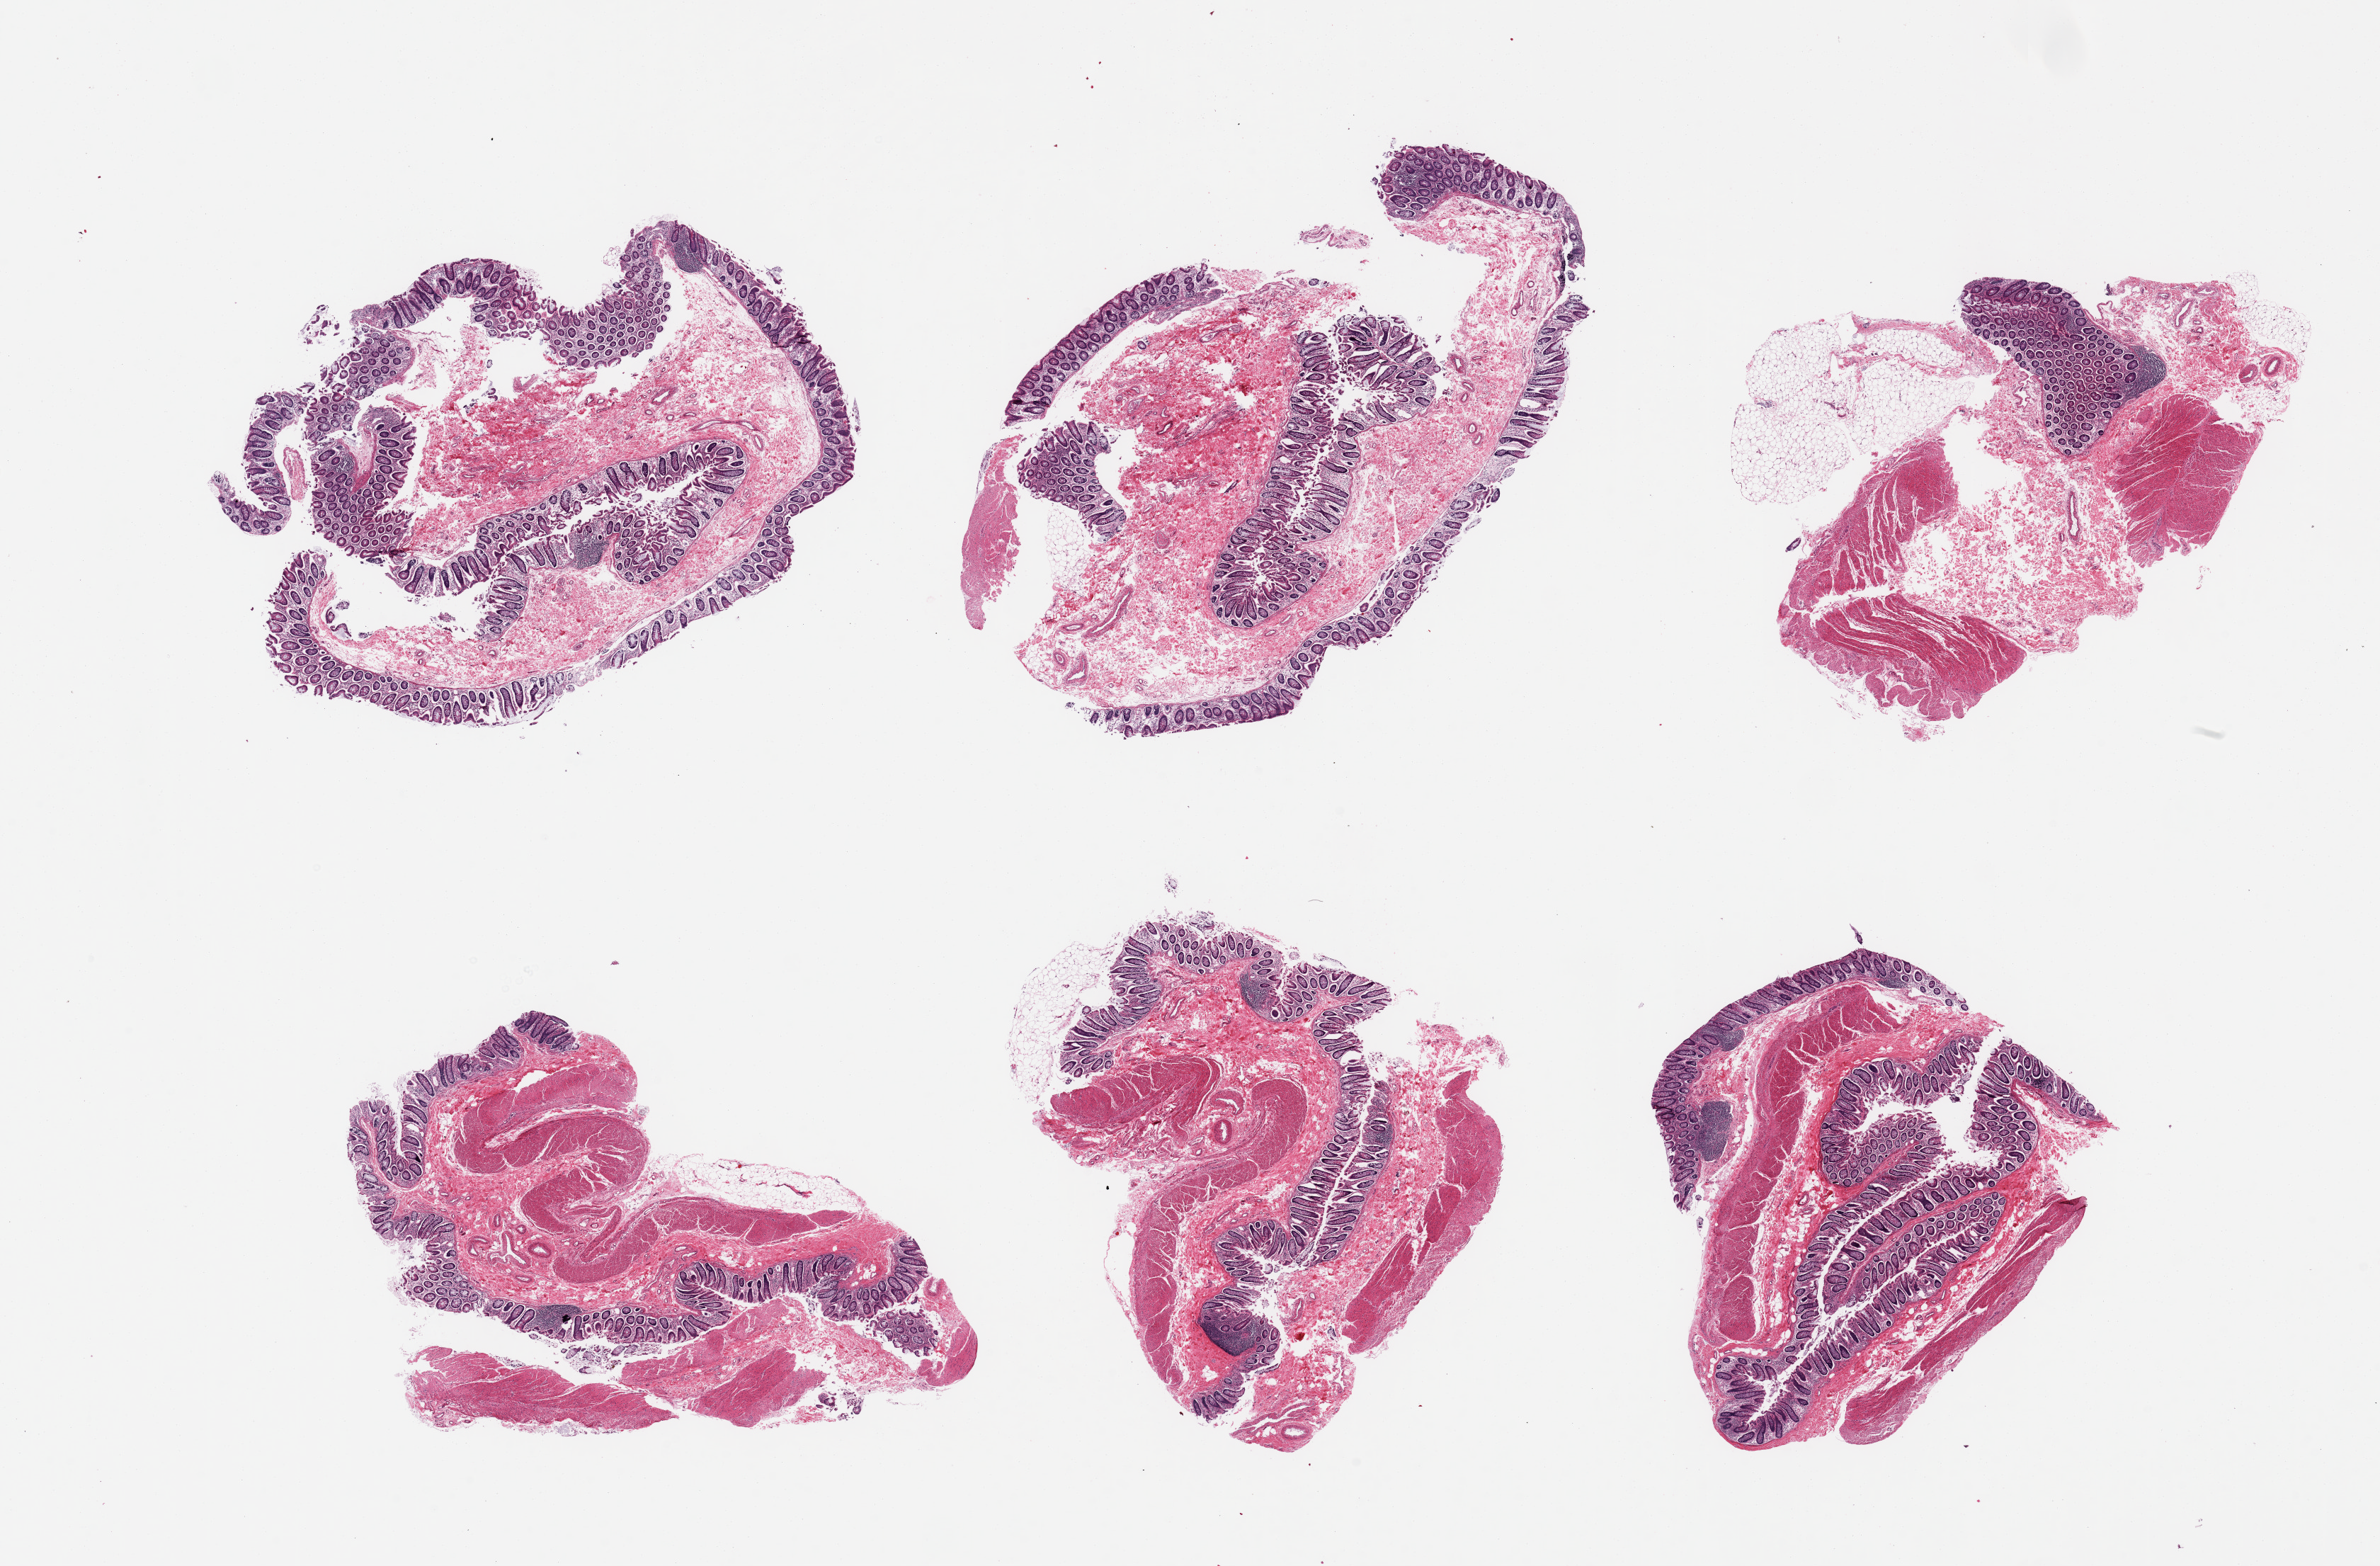
Digitized hematoxylin and eosin (H&E)-stained section, brightfield — a low-resolution overview of the entire scanned area, about 26.6 x 17.5 mm (slide scanned at 20x). PAXgene-fixed paraffin-embedded (PFPE) section. Sampled site (target tissue): transverse colon. Tissue donor sample.
Reviewer comment on this tissue sample: 6 pieces; 2 without muscularis.